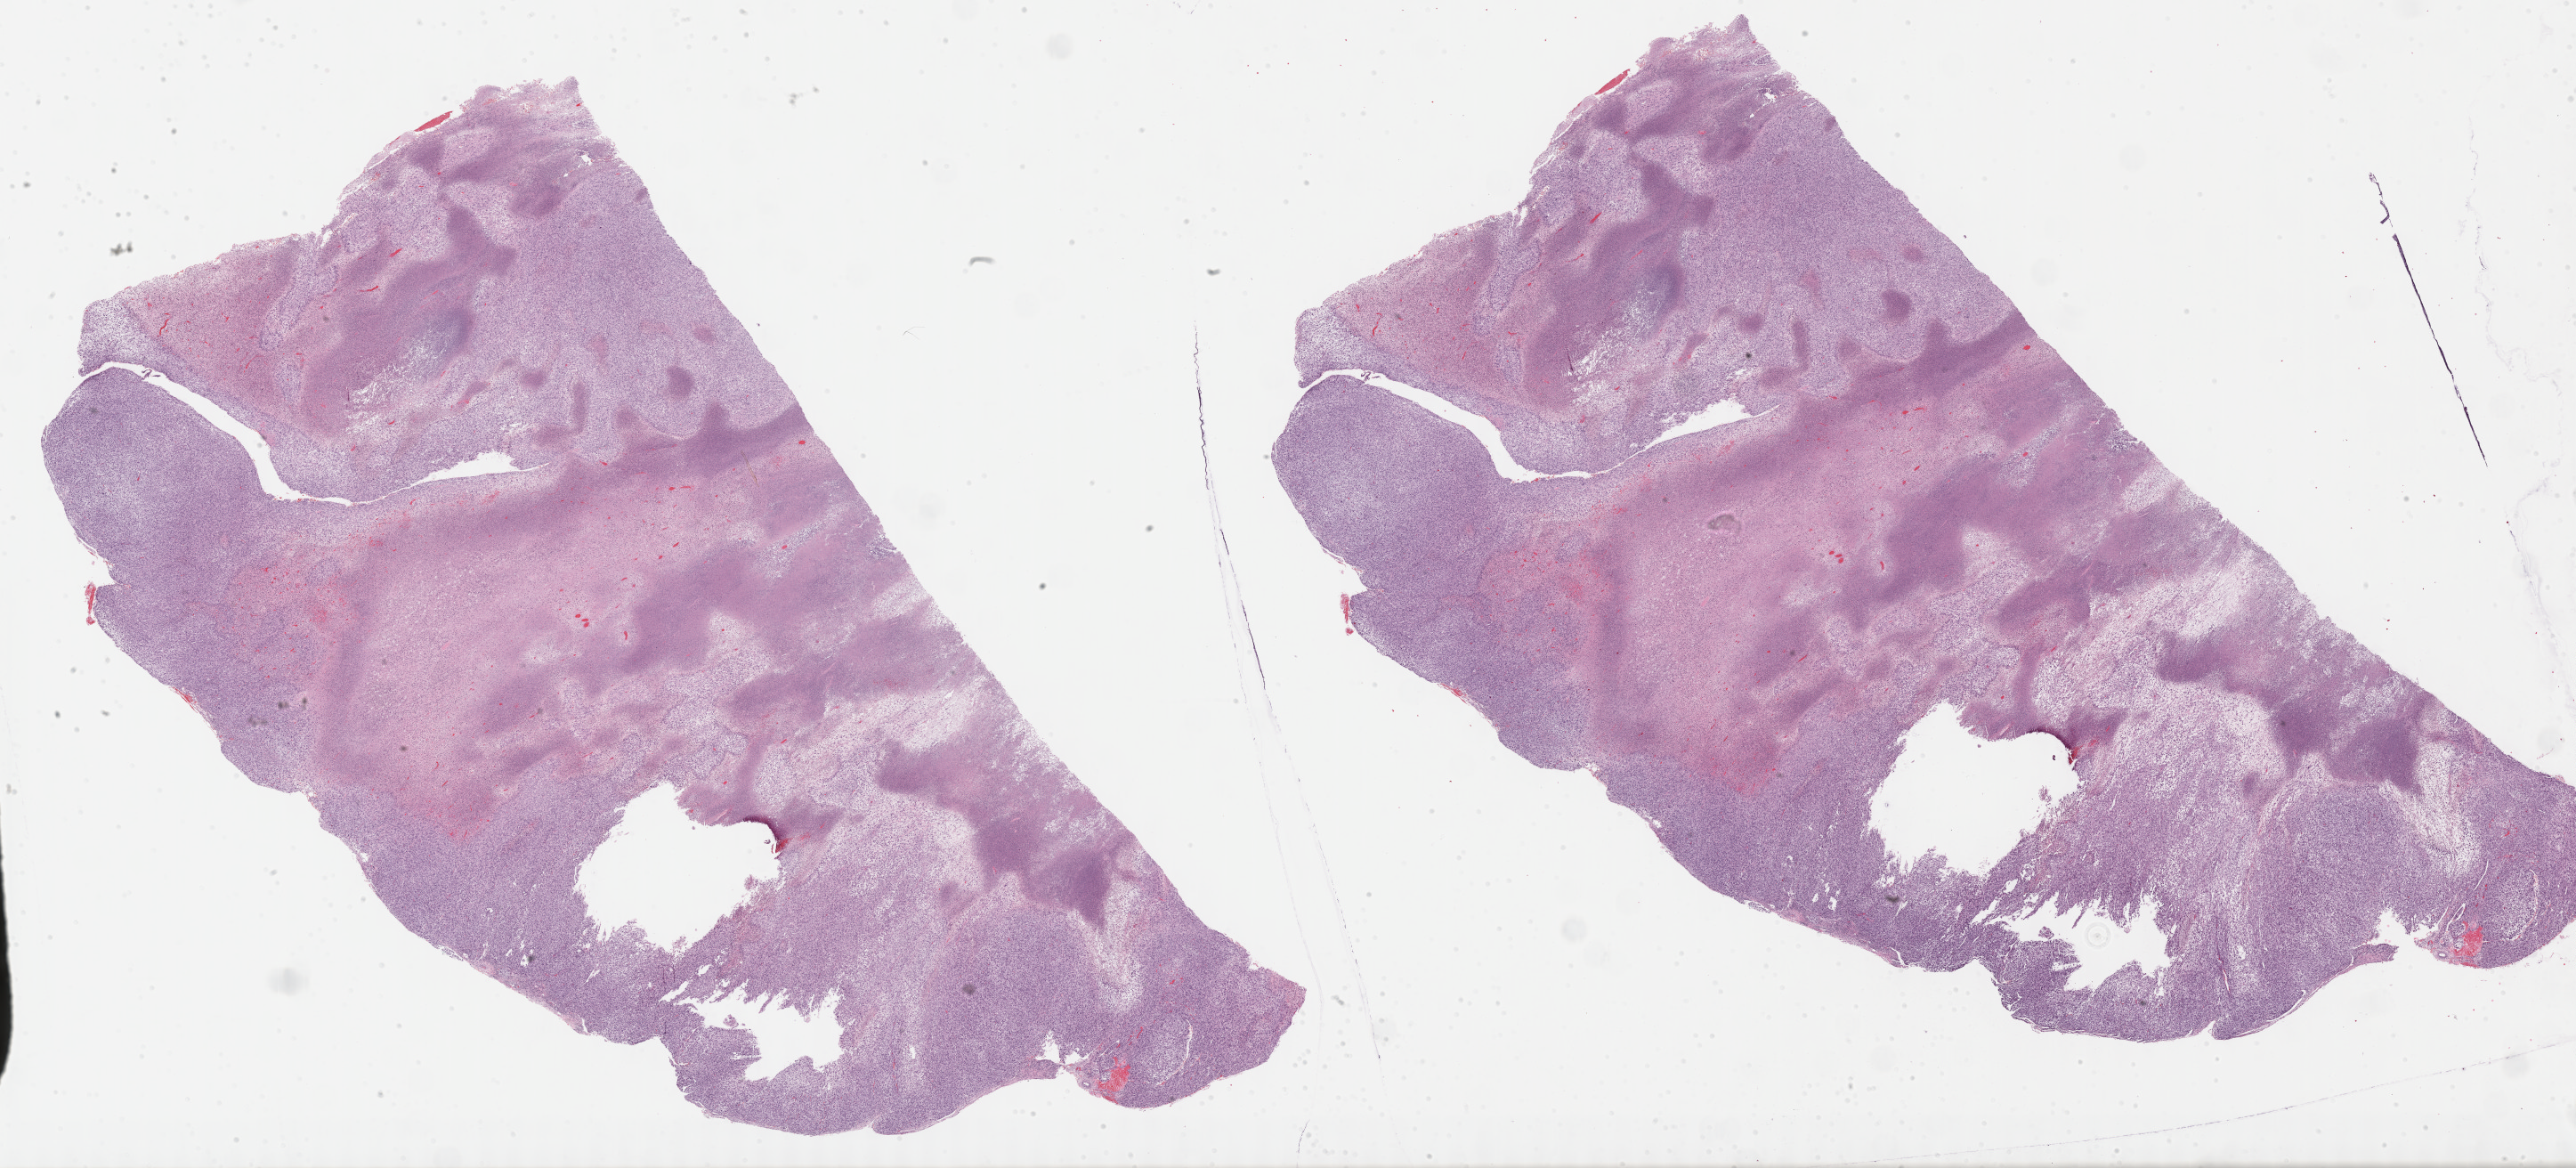
Digitized H&E-stained tissue section (whole slide), whole scanned area (about 46.8 x 21.2 mm) shown as a low-resolution overview. Formalin-fixed paraffin-embedded (FFPE) diagnostic section. Sample: primary tumour, connective, subcutaneous and other soft tissues. Patient: male, age at initial diagnosis 60 years.
* diagnosis: Fibromyxosarcoma (connective, subcutaneous and other soft tissues of thorax)